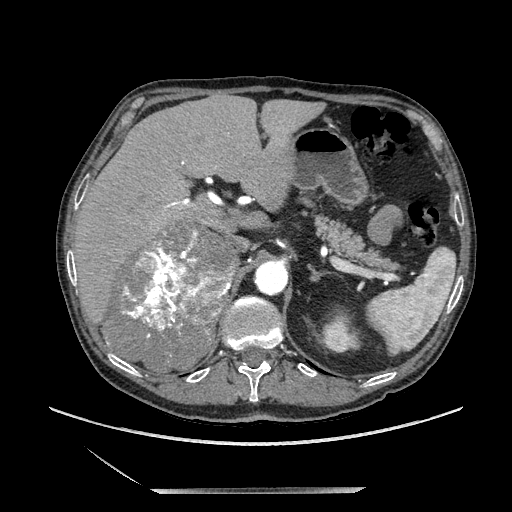
Contrast-enhanced abdominal CT, one axial slice; soft-tissue window (W 400 / L 40 HU); 1.25 mm slice thickness; 512 × 512 image matrix, field of view 420 × 420 mm. Male patient. From the clinical record (not read from this slice): diagnosis: adrenocortical carcinoma; tumour side: right adrenal; tumour size at pathology: 16 cm; Ki-67 index: 17 %; stage (as recorded): 3.
Annotated regions visible in this slice (semi-automatic segmentation, software-assisted and operator-edited):
- mass: box from (x=104, y=226) to (x=233, y=371) px